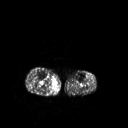
FDG PET of an extremity soft-tissue mass (from a PET/CT study), one axial slice. Position 148 of 267 along the scan axis. 3.27 mm slice thickness. 128 × 128 image matrix. Patient: male, 69 years. From the clinical record (not read from this slice): histological type: pleiomorphic liposarcoma; grade: high; site of the primary tumour: right calf.
Outlined on this slice (expert contour drawn on MRI and transferred to this co-registered scan by the dataset authors):
- gross tumour volume including surrounding oedema: bounding box (x1, y1, x2, y2) in pixels: (55, 80, 57, 84)